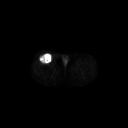
FDG PET of an extremity soft-tissue mass (from a PET/CT study), one axial slice; slice 273 of 311 in the series (ordered by position); 3.27 mm slice thickness; 128 × 128 image matrix. Patient: male, 56 years. Case-level facts recorded for this patient, not image findings: histological type: pleiomorphic leiomyosarcoma; grade: intermediate; site of the primary tumour: right thigh.
Annotated regions visible in this slice (expert contour drawn on MRI and transferred to this co-registered scan by the dataset authors):
- gross tumour volume including surrounding oedema: bounding box (x1, y1, x2, y2) in pixels: (39, 54, 52, 64)
- gross tumour volume (mass): (39, 54, 52, 64)